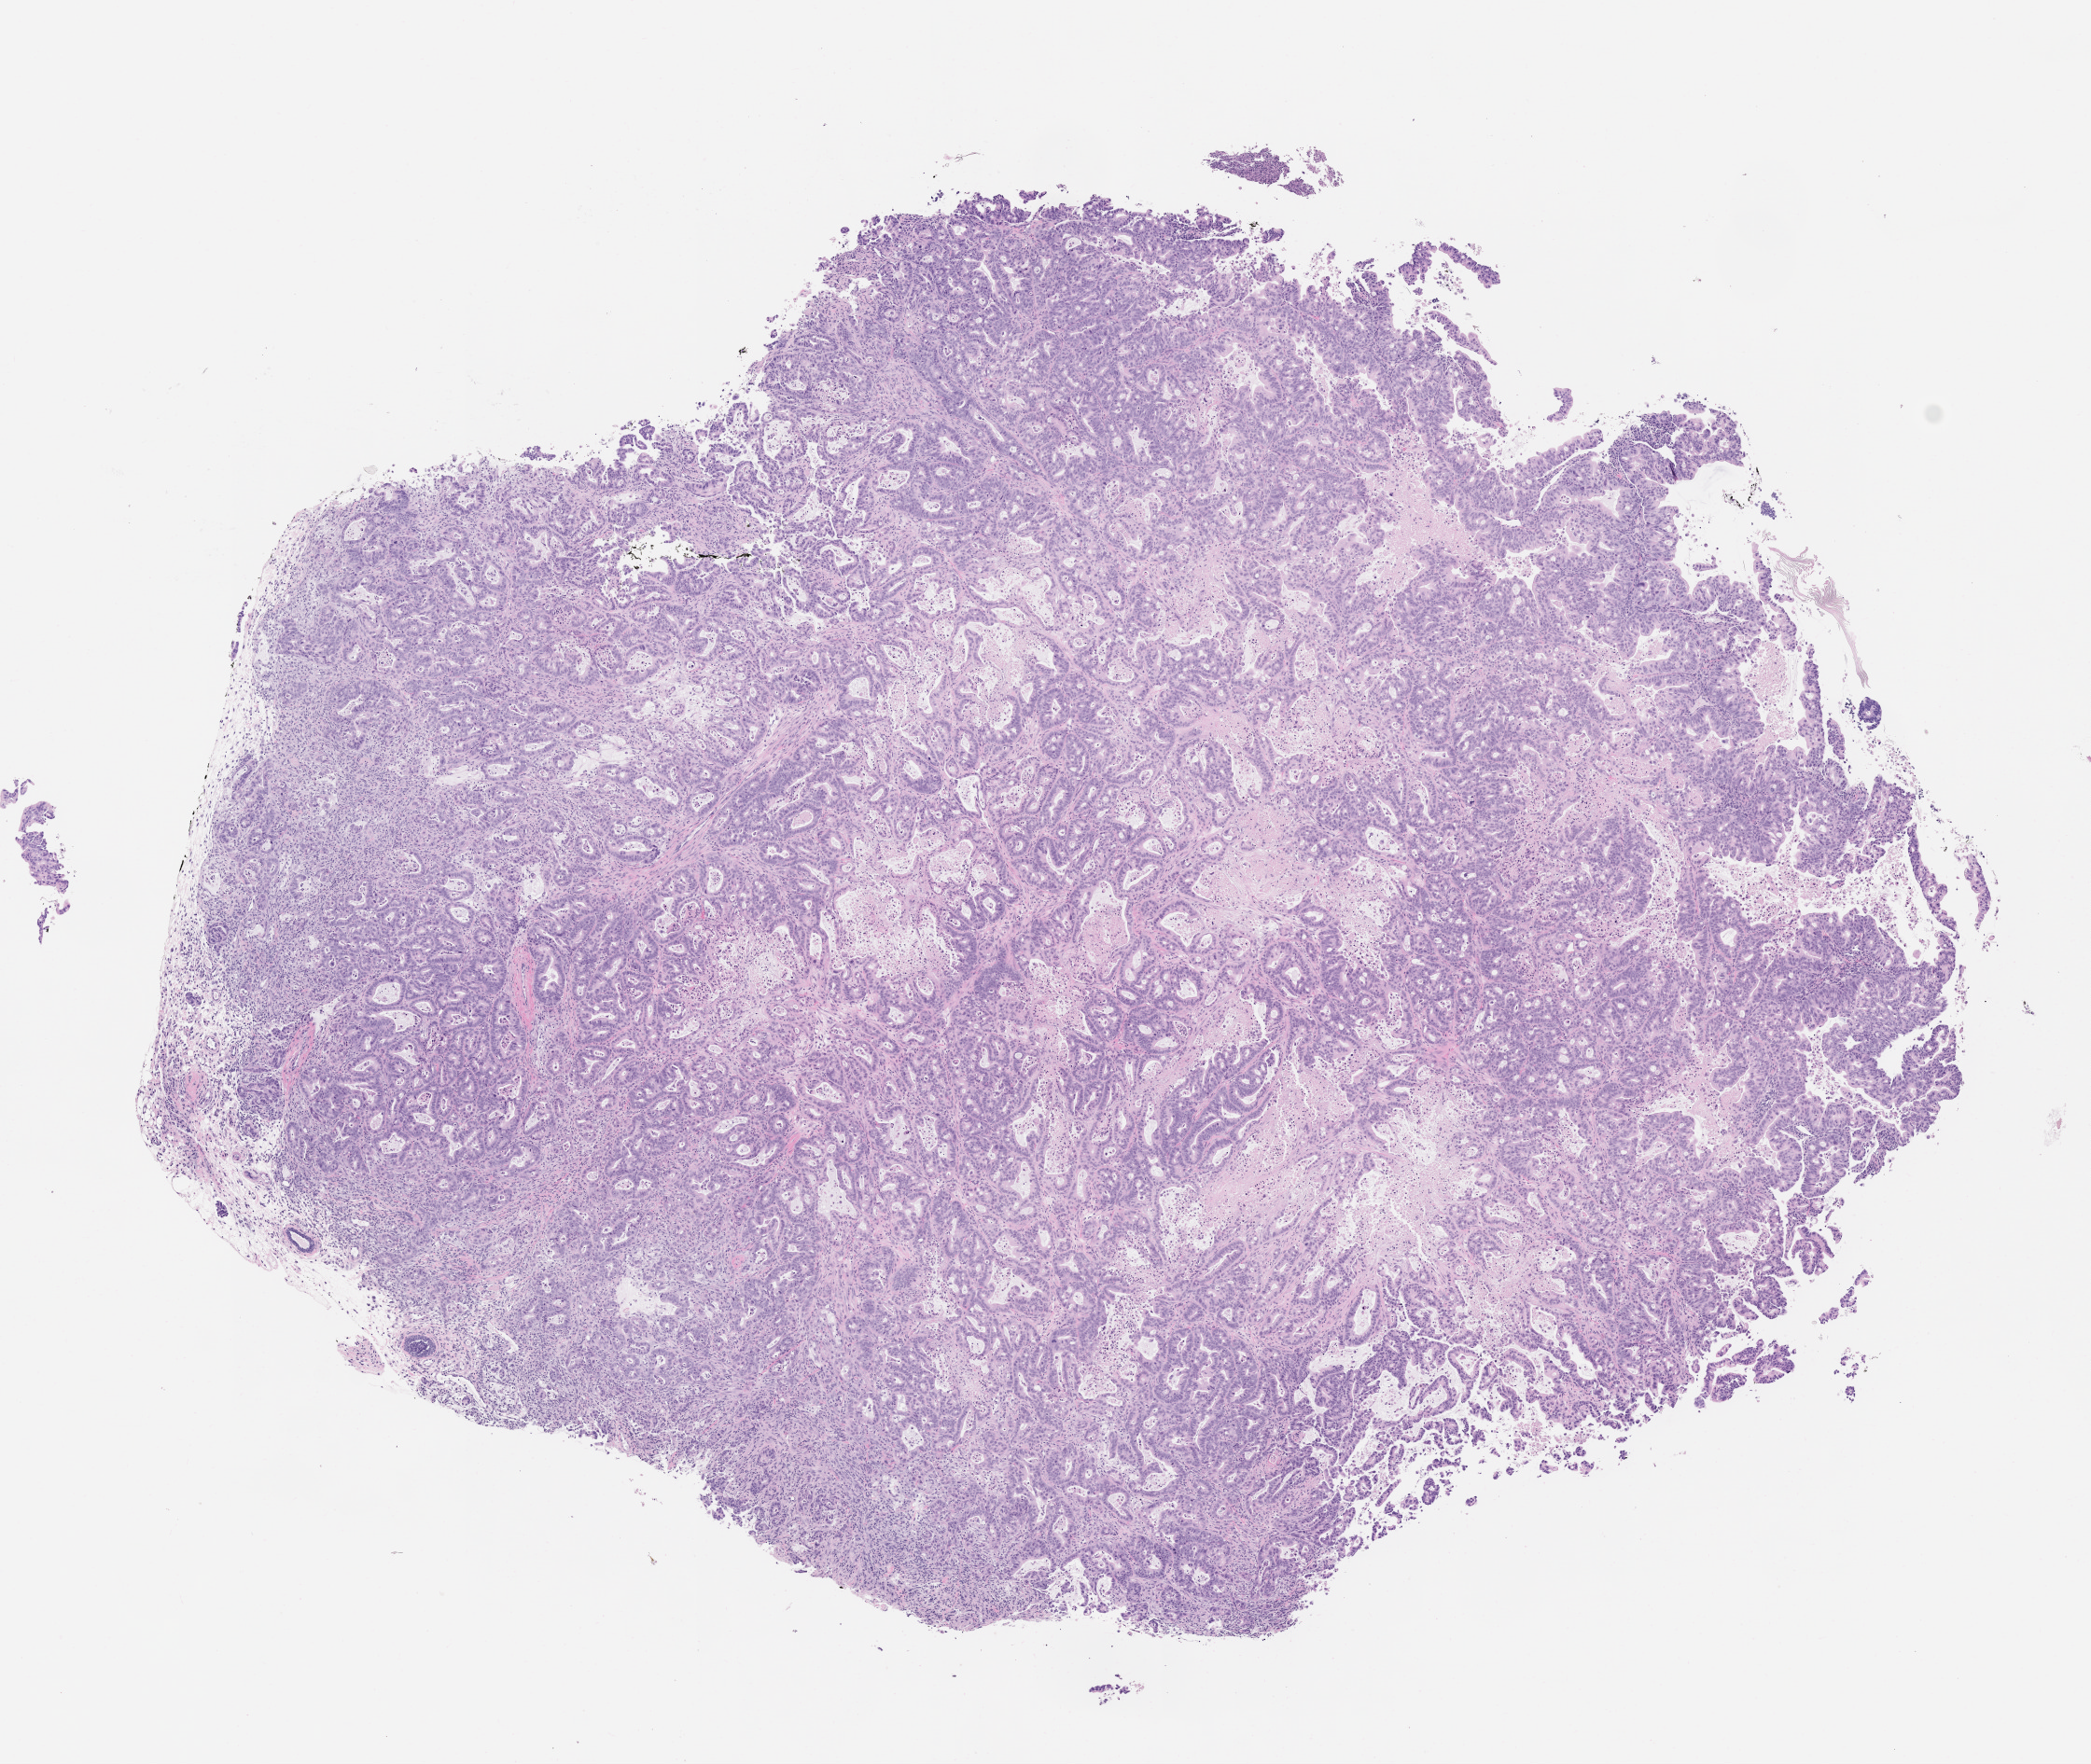
Hematoxylin and eosin (H&E) whole-slide image of a patient-derived xenograft (PDX) tumor grown in a mouse, passage 3 — shown as a low-resolution overview of the whole scanned area (about 9.0 x 7.6 mm), formalin-fixed paraffin-embedded section, tumor site category: pancreas.
Originating patient diagnosis: Pancreatic Adenocarcinoma.